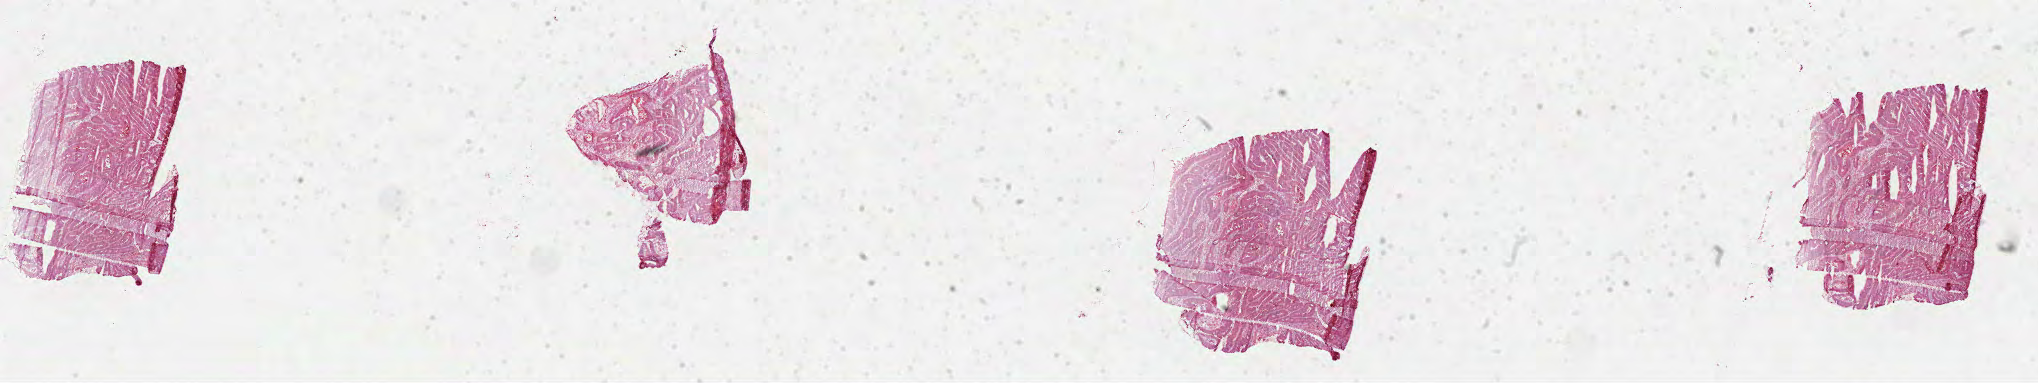
H&E whole-slide image, whole scanned area (about 32.9 x 6.2 mm, slide scanned at 40x) shown as a low-resolution overview, formalin-fixed paraffin-embedded (FFPE) diagnostic section, rectum, primary tumour sample. Patient: male, age at initial diagnosis 60 years.
Diagnosis: Adenocarcinoma in tubulovillous adenoma. AJCC pathologic stage: IIIA (6th edition).